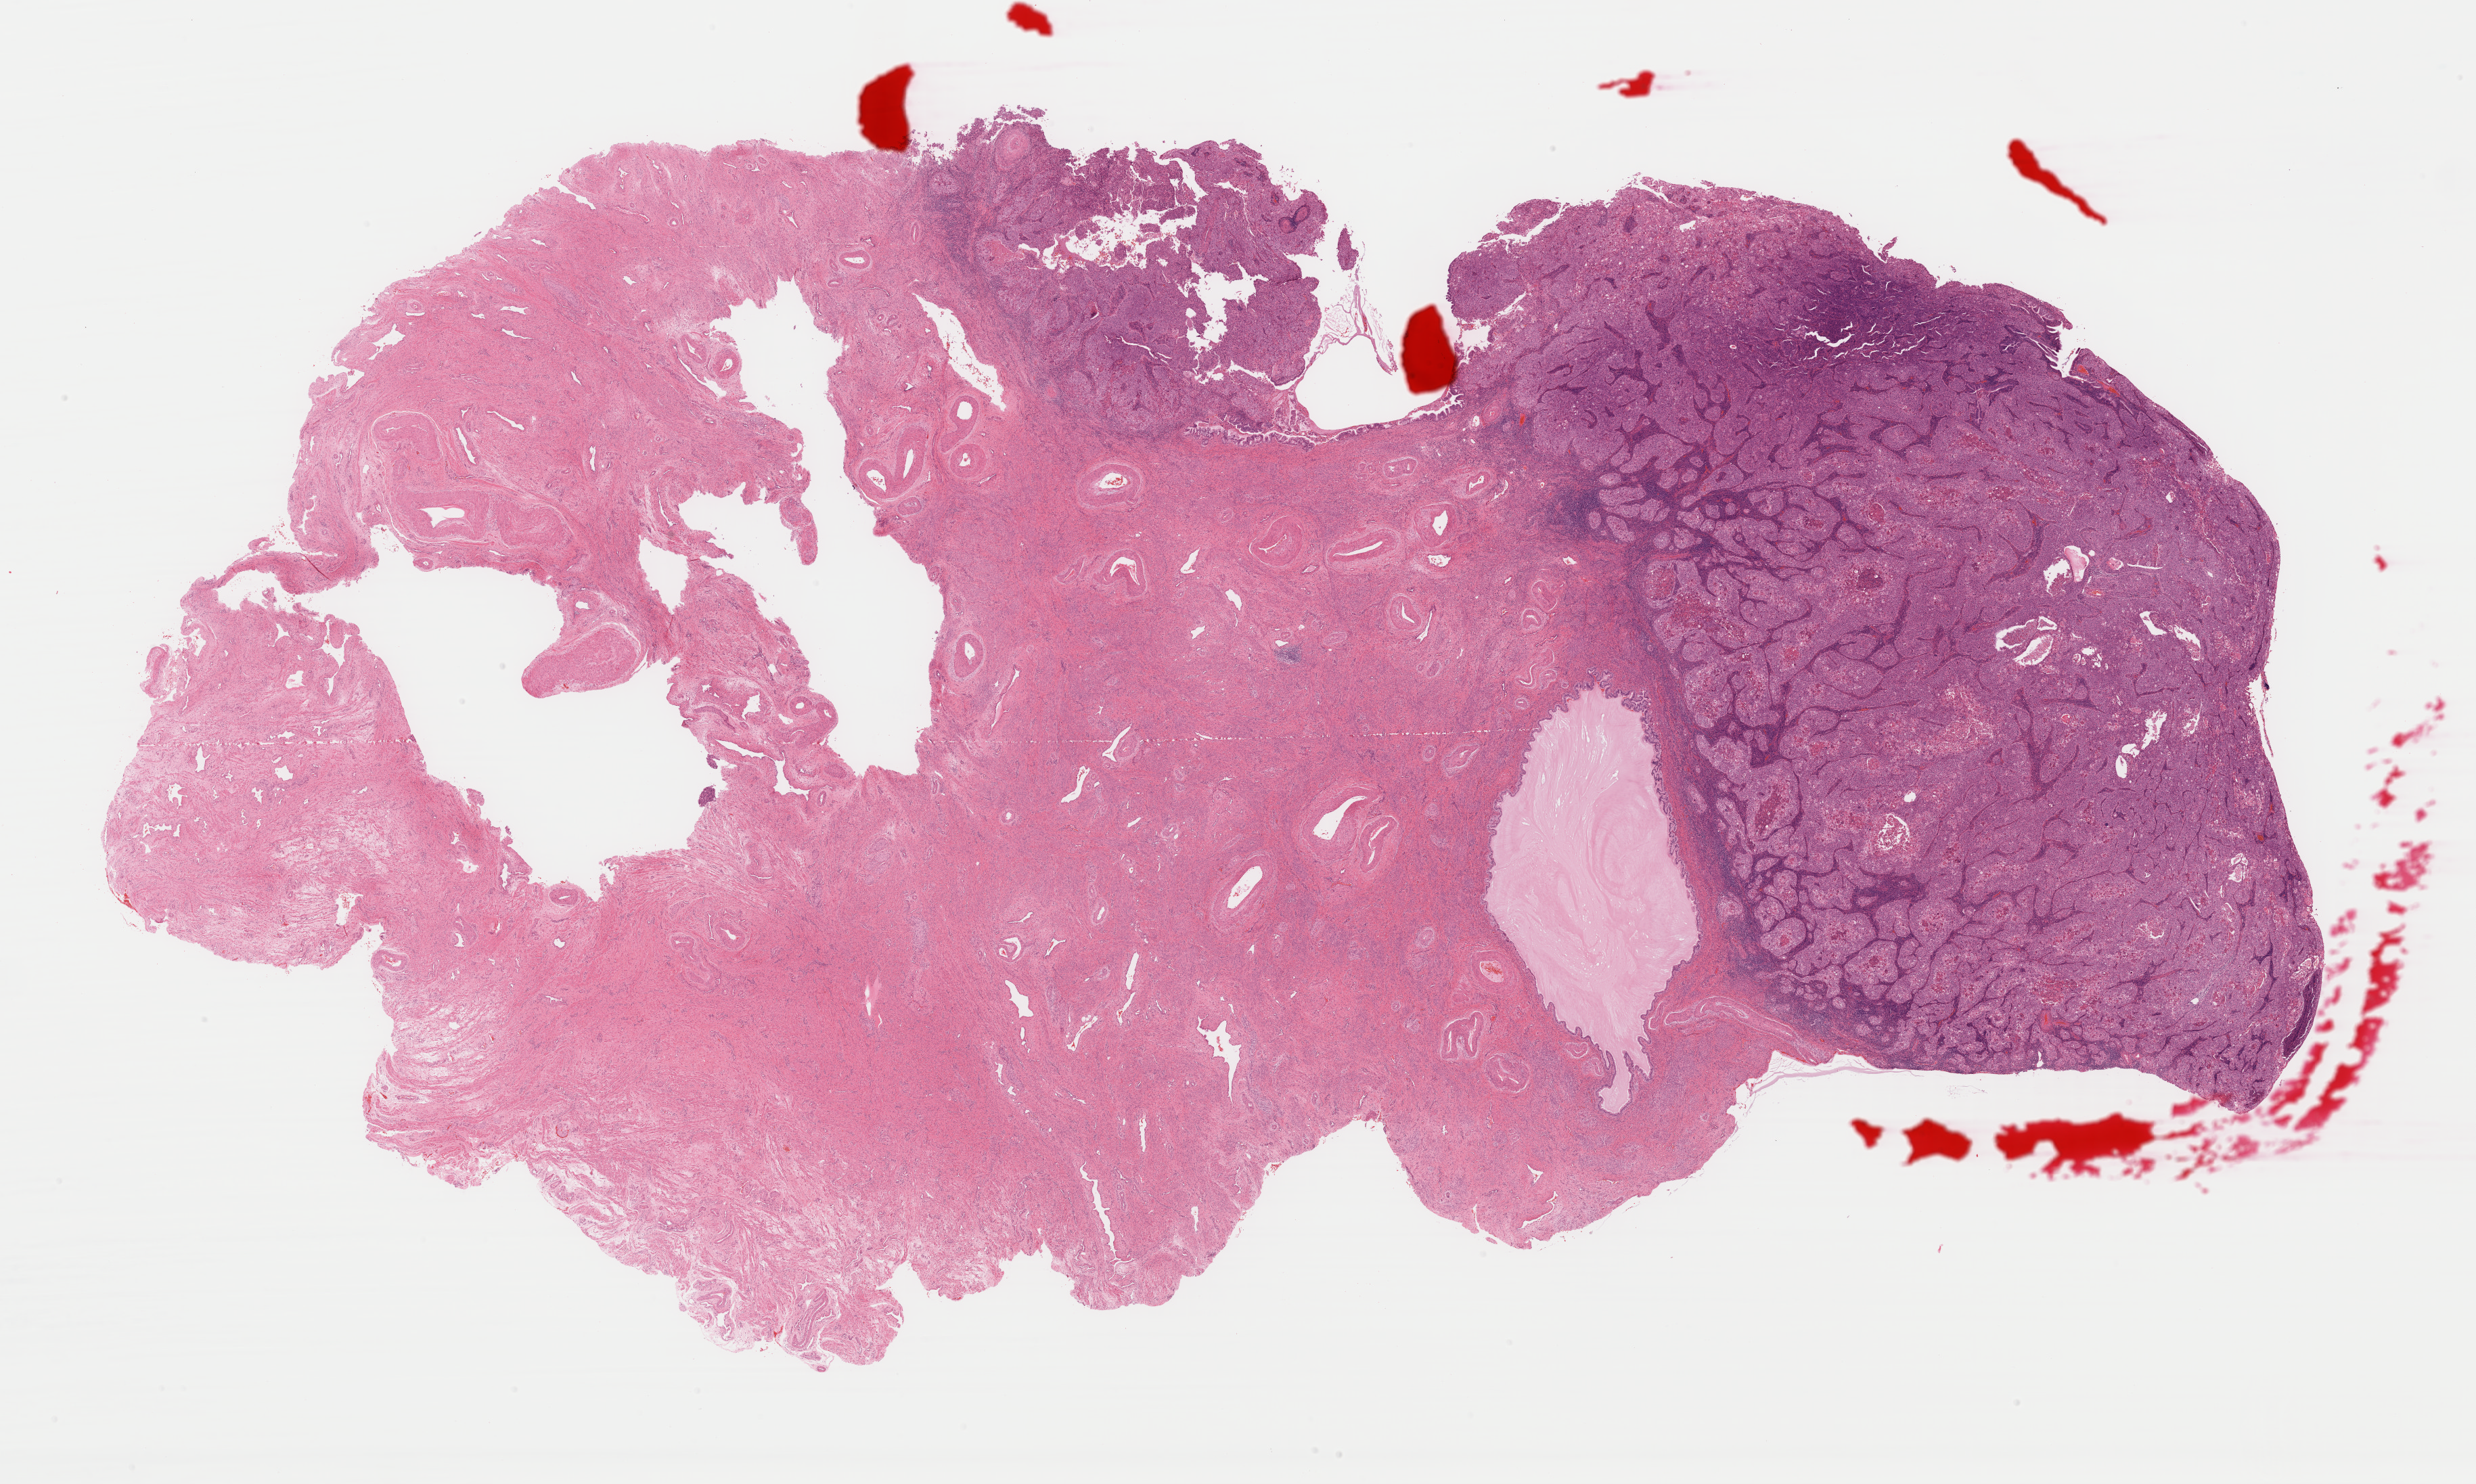
Digitized H&E tissue section (whole slide) — whole scanned area (about 28.9 x 17.3 mm, acquisition: 40x scan) shown as a low-resolution overview, formalin-fixed paraffin-embedded (FFPE) diagnostic section, cervix, primary tumour sample. Patient: female, age at initial diagnosis 43 years. Histologic grade: G2 (moderately differentiated).
Pathologic diagnosis: Squamous cell carcinoma, keratinizing, NOS. Lymph nodes positive (case pathology): 0 of 24 examined. FIGO stage: IB1.